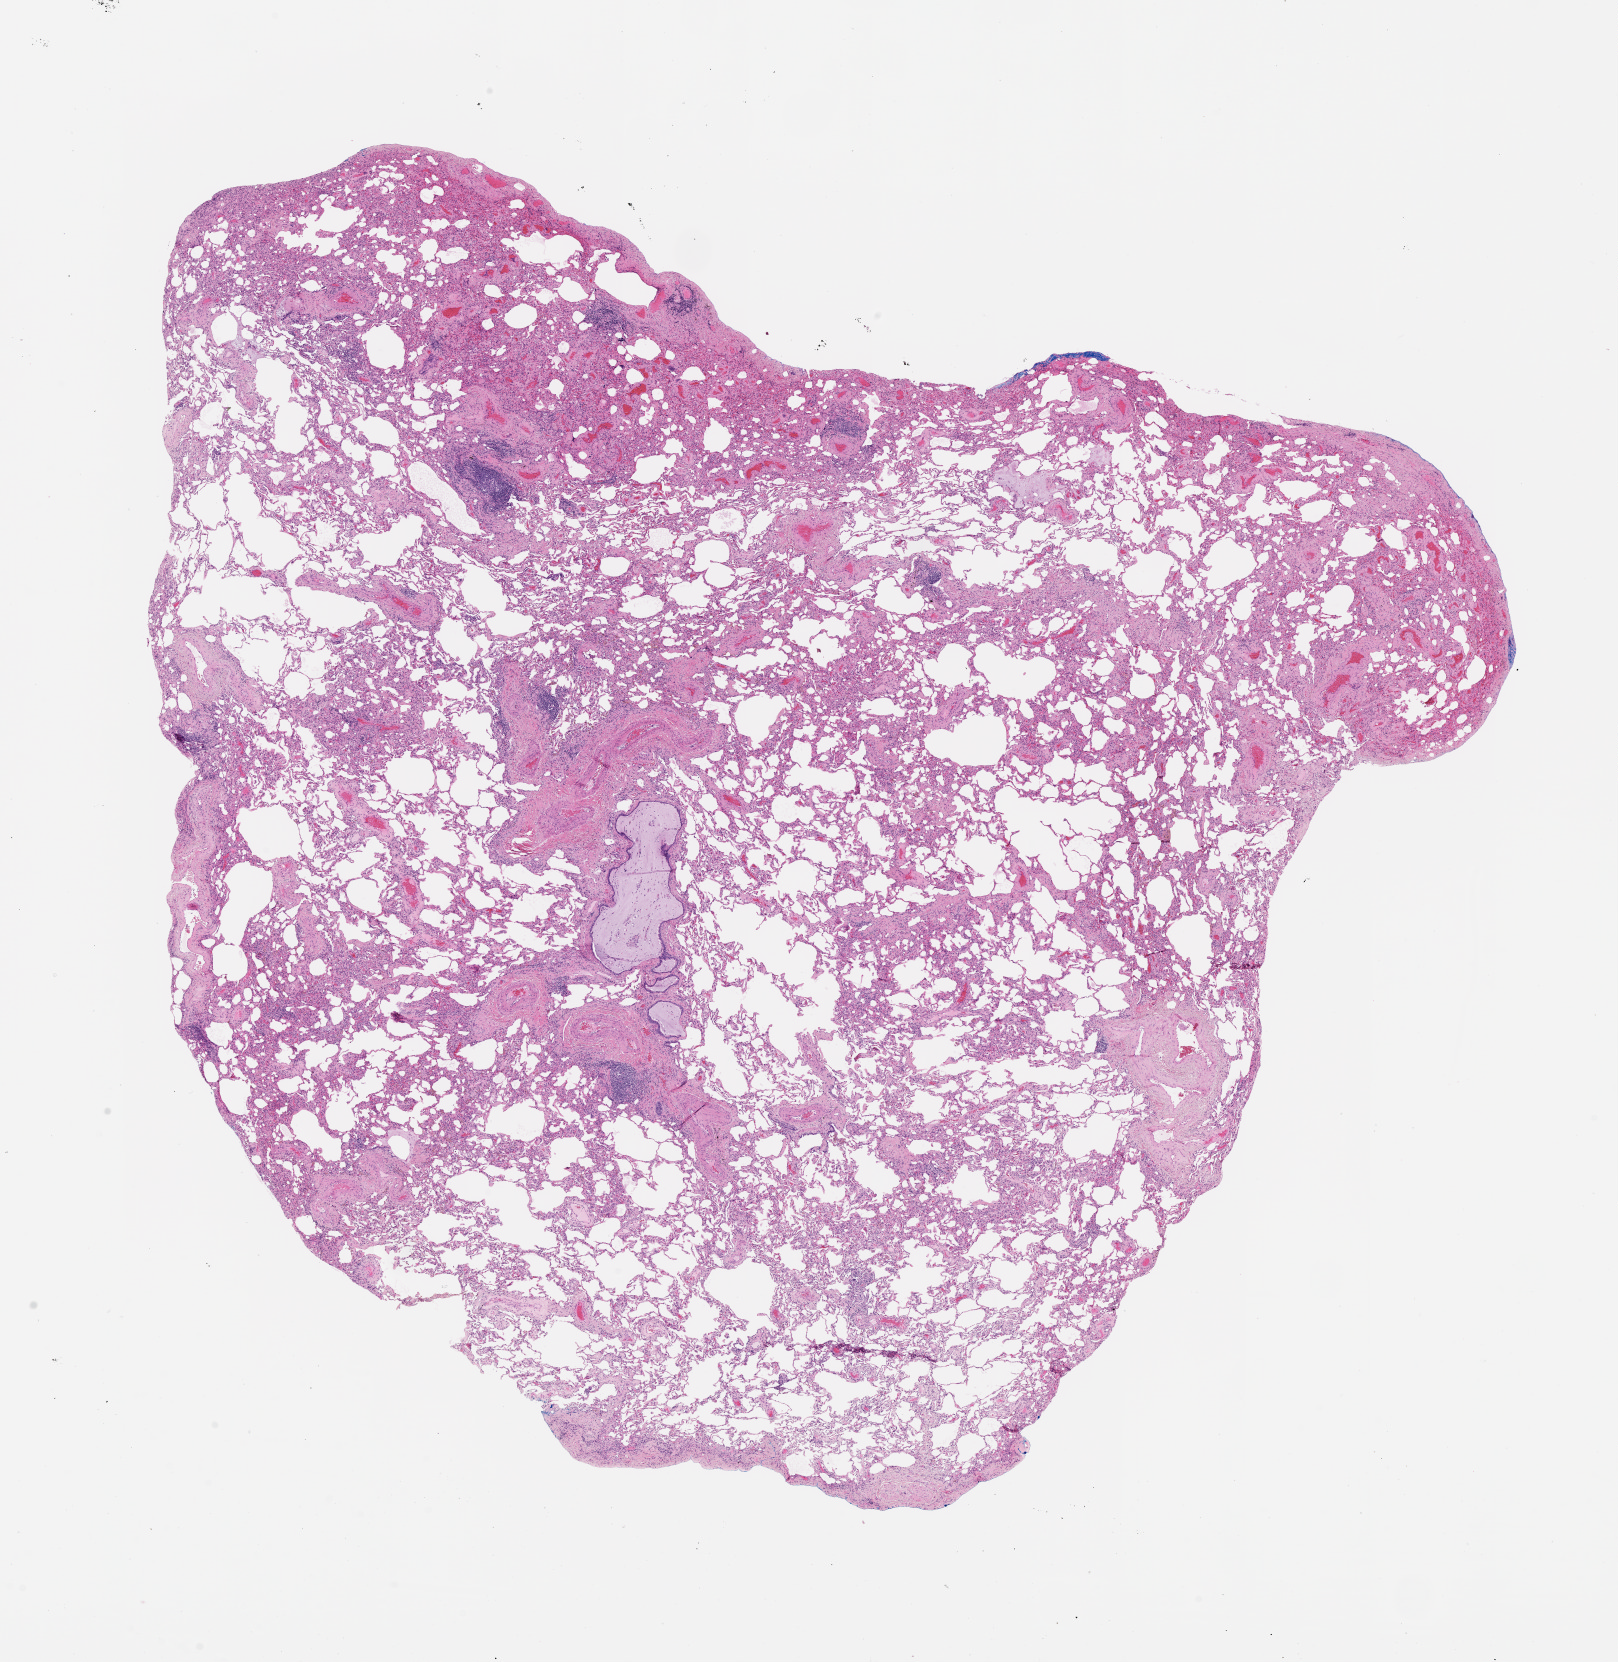
Whole-slide histology image, H&E-stained, a low-resolution overview of the entire scanned area, about 13.0 x 13.4 mm. Normal (non-tumour) tissue sample, lung. Male, 56 y/o.
* this section: normal (non-tumour) tissue from the same patient
* patient diagnosis (cohort enrolment): squamous cell carcinoma (lung)